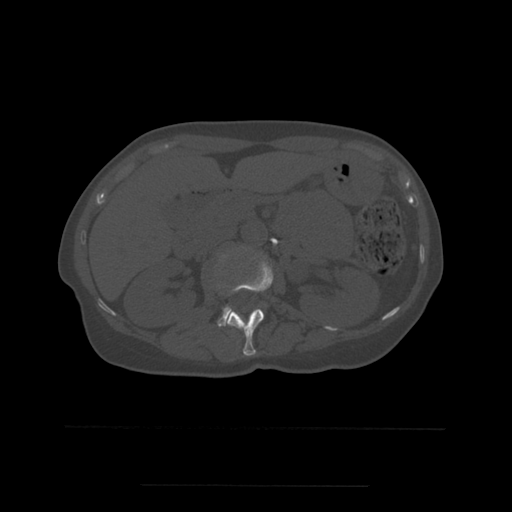
CT including the spine, one axial slice; position 226 of 544 along the scan axis; bone window (W 1800 / L 400 HU); 512 × 512 image matrix, field of view 350 × 350 mm. Patient age 58 years. From the clinical record (not read from this slice): primary cancer: lung.
Structures marked on this image (semi-automatic segmentation, software-assisted and operator-edited):
- L1 vertebra: bounding box [x1, y1, x2, y2] px = [226, 261, 274, 356]
- L2 vertebra: [218, 307, 263, 327]